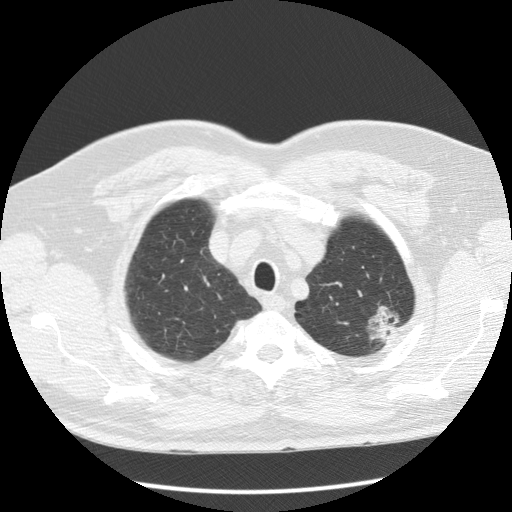
Axial slice from a low-dose chest CT screening exam; baseline annual screen; lung window (W 1500 / L -600 HU); 2.5 mm slice thickness; slice 18 of 123 in the series. Male, age 60 years at enrolment.
- Expert reader's lesion annotation, bounding box <350,295,413,355> (left, top, right, bottom; pixels).
- The screening reader recorded 3 non-calcified nodules or masses ≥4 mm on this exam (left upper lobe, right upper lobe, left upper lobe); which of them this box marks is not recorded.
- Later outcome: lung cancer diagnosed 48 days after this screen — bronchiolo-alveolar adenocarcinoma, NOS, left upper lobe, well differentiated (G1), stage IA (AJCC 6th edition), 27 mm at pathology.